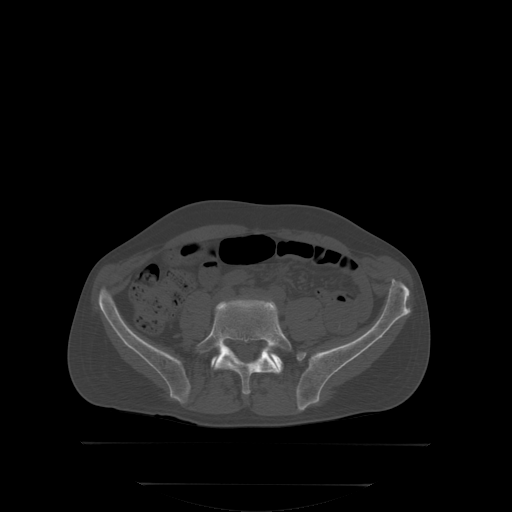
CT including the spine, one axial slice. Position 95 of 350 along the scan axis. Bone window (W 1800 / L 400 HU). 512 × 512 image matrix. Patient: male, 58 years. From the clinical record (not read from this slice): primary cancer: prostate.
Annotated regions visible in this slice (semi-automatically segmented with operator editing):
- L5 vertebra: box from (x=195, y=300) to (x=292, y=394) px